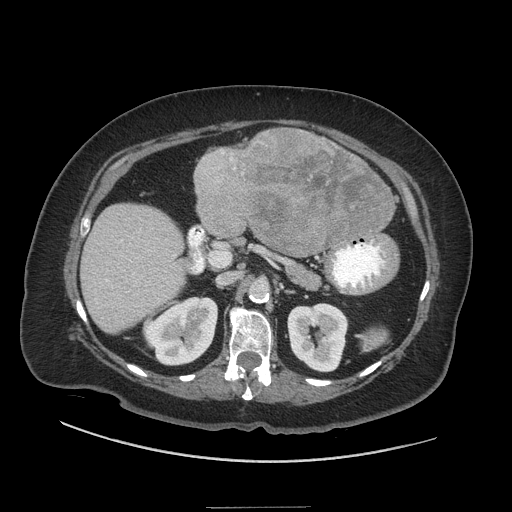
Contrast-enhanced abdominal CT (liver protocol), one axial slice. Position 15 of 81 along the scan axis. Soft-tissue window (W 400 / L 40 HU). 2.5 mm slice thickness. 512 × 512 image matrix, field of view 440 × 440 mm. From the clinical record (not read from this slice): diagnosis: hepatocellular carcinoma (patient treated with transarterial chemoembolisation; whether this scan precedes or follows treatment is not stated here); TNM stage (as recorded): Stage-II; Child-Pugh class: A; tumour nodularity: multinodular; tumour size: 1.7 cm.
Structures marked on this image (semi-automatic segmentation, software-assisted and operator-edited):
- liver parenchyma outside the tumour (the mass and vessels are separate outlines, so this box may not span the whole liver): bounding box <80,130,396,332> (left, top, right, bottom; pixels)
- mass: <192,128,397,255>
- liver vessels: <105,230,175,282>